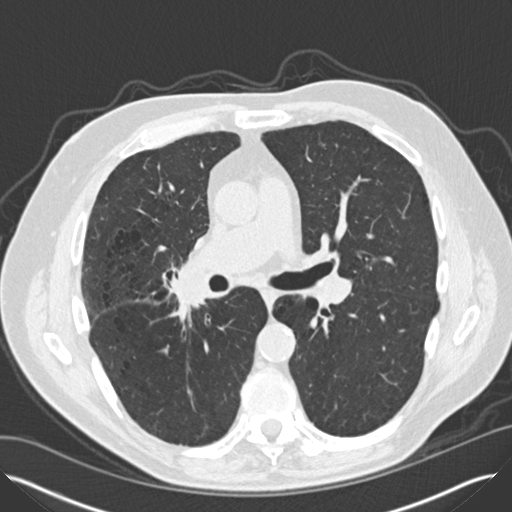
Axial slice from a low-dose chest CT screening exam. Second annual screen. Lung window (W 1500 / L -600 HU). Slice 69 of 149 in the series. Male, age 65 years at enrolment. Current smoker at enrolment.
Expert reader's lesion annotation, bounding box [x1, y1, x2, y2] px = [153, 263, 211, 315]. Reader record for this screening exam (exam-level; its link to the box is not recorded): non-calcified nodule or mass ≥4 mm, left lower lobe, 12 × 8 mm, smooth margins, soft tissue attenuation, pre-existing on the prior screen: yes; interval growth: yes. Note: the box lies in the patient's right hemithorax on this image, whereas the reader's record names the left lung; they may be different findings. Lung cancer was diagnosed 67 days after this screen: non-small cell carcinoma, left lower lobe, right hilum, poorly differentiated (G3), stage IV (AJCC 6th edition), 5 mm at pathology.